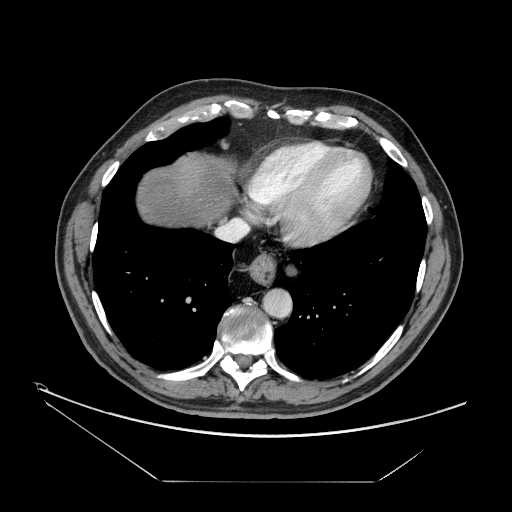
Contrast-enhanced abdominal CT, one axial slice. Position 150 of 161 along the scan axis. Reconstruction kernel STANDARD. 120 kVp. Soft-tissue window (W 400 / L 40 HU). 2.5 mm slice thickness. 512 × 512 image matrix, field of view 440 × 440 mm. Male patient, age 65 years. From the clinical record (not read from this slice): diagnosis: colorectal cancer liver metastases, imaged before liver resection; multiple liver metastases: yes; largest metastasis: 4.2 cm.
Structures marked on this image (manually delineated by an expert):
- hepatic veins: bounding box <217,164,267,241> (left, top, right, bottom; pixels)
- liver: <137,153,232,226>
- planned liver remnant (the part of the liver to remain after resection): <137,153,232,226>